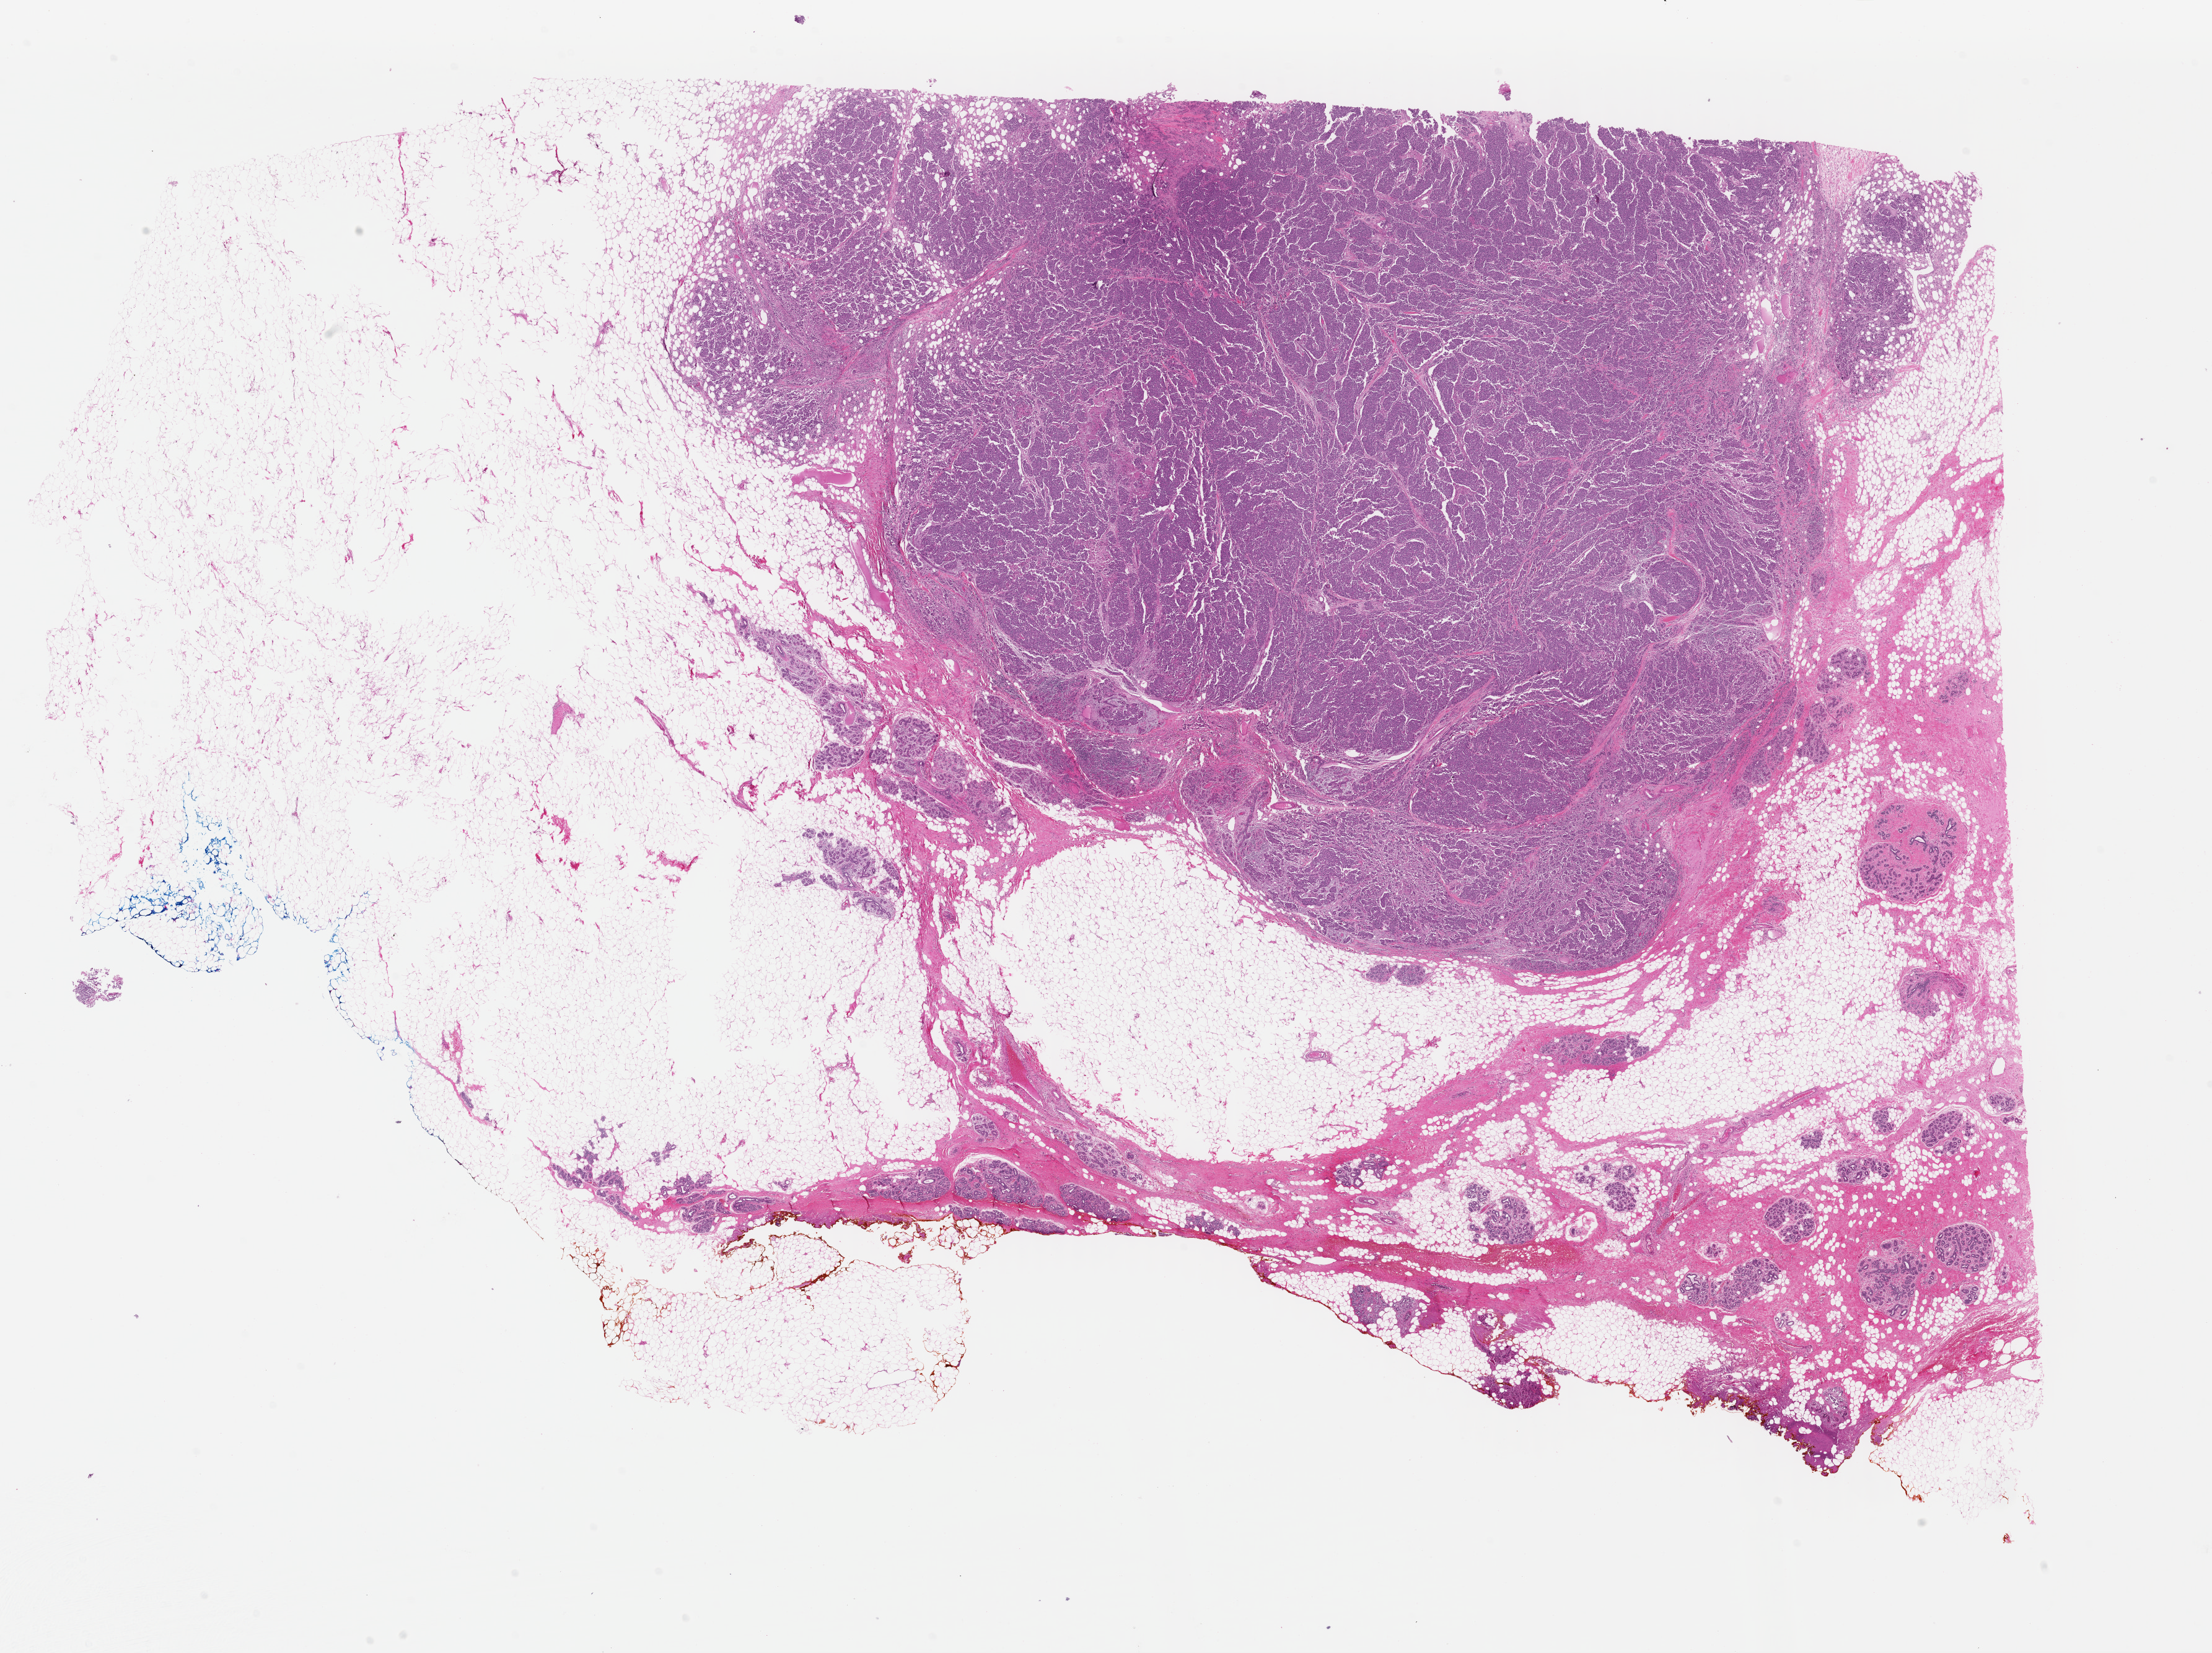
Digitized H&E-stained tissue section (whole slide) — low-resolution overview of the scanned area, about 28.1 x 21.0 mm (from a 40x scan). Formalin-fixed paraffin-embedded (FFPE) diagnostic section. Breast, primary tumour sample. Female patient; age at initial diagnosis 45 years.
Diagnosis: Infiltrating duct carcinoma, NOS.